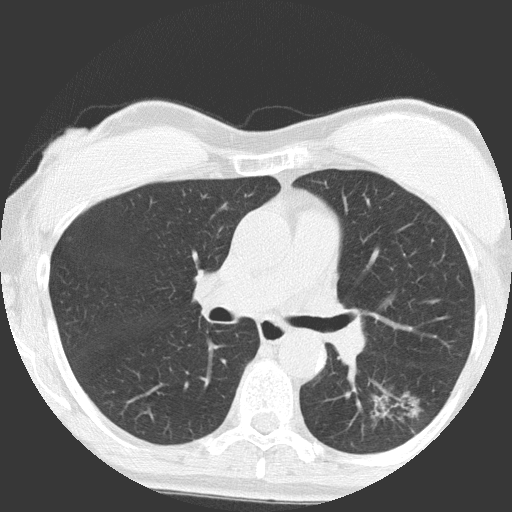
Chest CT (low-dose screening protocol), one axial image. Baseline annual screen. Lung window (W 1500 / L -600 HU). 2 mm slice thickness. Slice 61 of 149 in the series. 512 × 512 image matrix, field of view 300 × 300 mm. Female, age 64 years at enrolment. Former smoker at enrolment.
Lesion marked by an expert reader, bounding box [x1, y1, x2, y2] px = [349, 381, 434, 455]. The exam's reader record, not a measurement of the box and not confirmed to be the same lesion: non-calcified nodule or mass ≥4 mm, right upper lobe, 4 × 4 mm, poorly defined margins, ground glass attenuation. Note: the box lies in the patient's left hemithorax on this image, whereas the reader's record names the right lung; they may be different findings. Official screen result: positive, change unspecified: nodule(s) >= 4 mm or enlarging nodule(s), mass(es), or other non-specific abnormalities suspicious for lung cancer. Later outcome: lung cancer diagnosed 932 days after this screen (after the third annual screen) — adenocarcinoma, NOS, left lower lobe, moderately differentiated (G2), stage IA (AJCC 6th edition), 17 mm at pathology.